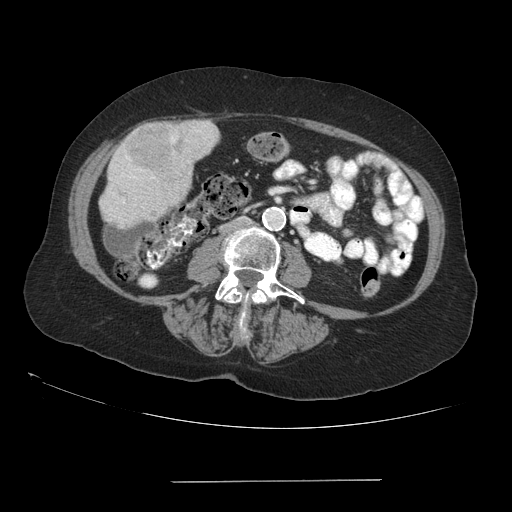
Contrast-enhanced abdominal CT (liver protocol), one axial slice. Position 21 of 89 along the scan axis. Reconstruction kernel STANDARD. 140 kVp. Soft-tissue window (W 400 / L 40 HU). 2.5 mm slice thickness. 512 × 512 image matrix. Case-level facts recorded for this patient, not image findings: diagnosis: hepatocellular carcinoma (patient treated with transarterial chemoembolisation; whether this scan precedes or follows treatment is not stated here); TNM stage (as recorded): Stage-IVA; Child-Pugh class: A; tumour nodularity: uninodular.
Outlined on this slice (semi-automatically segmented with operator editing):
- liver parenchyma outside the tumour (the mass and vessels are separate outlines, so this box may not span the whole liver): bounding box <100,120,218,228> (left, top, right, bottom; pixels)
- mass: <124,123,171,165>